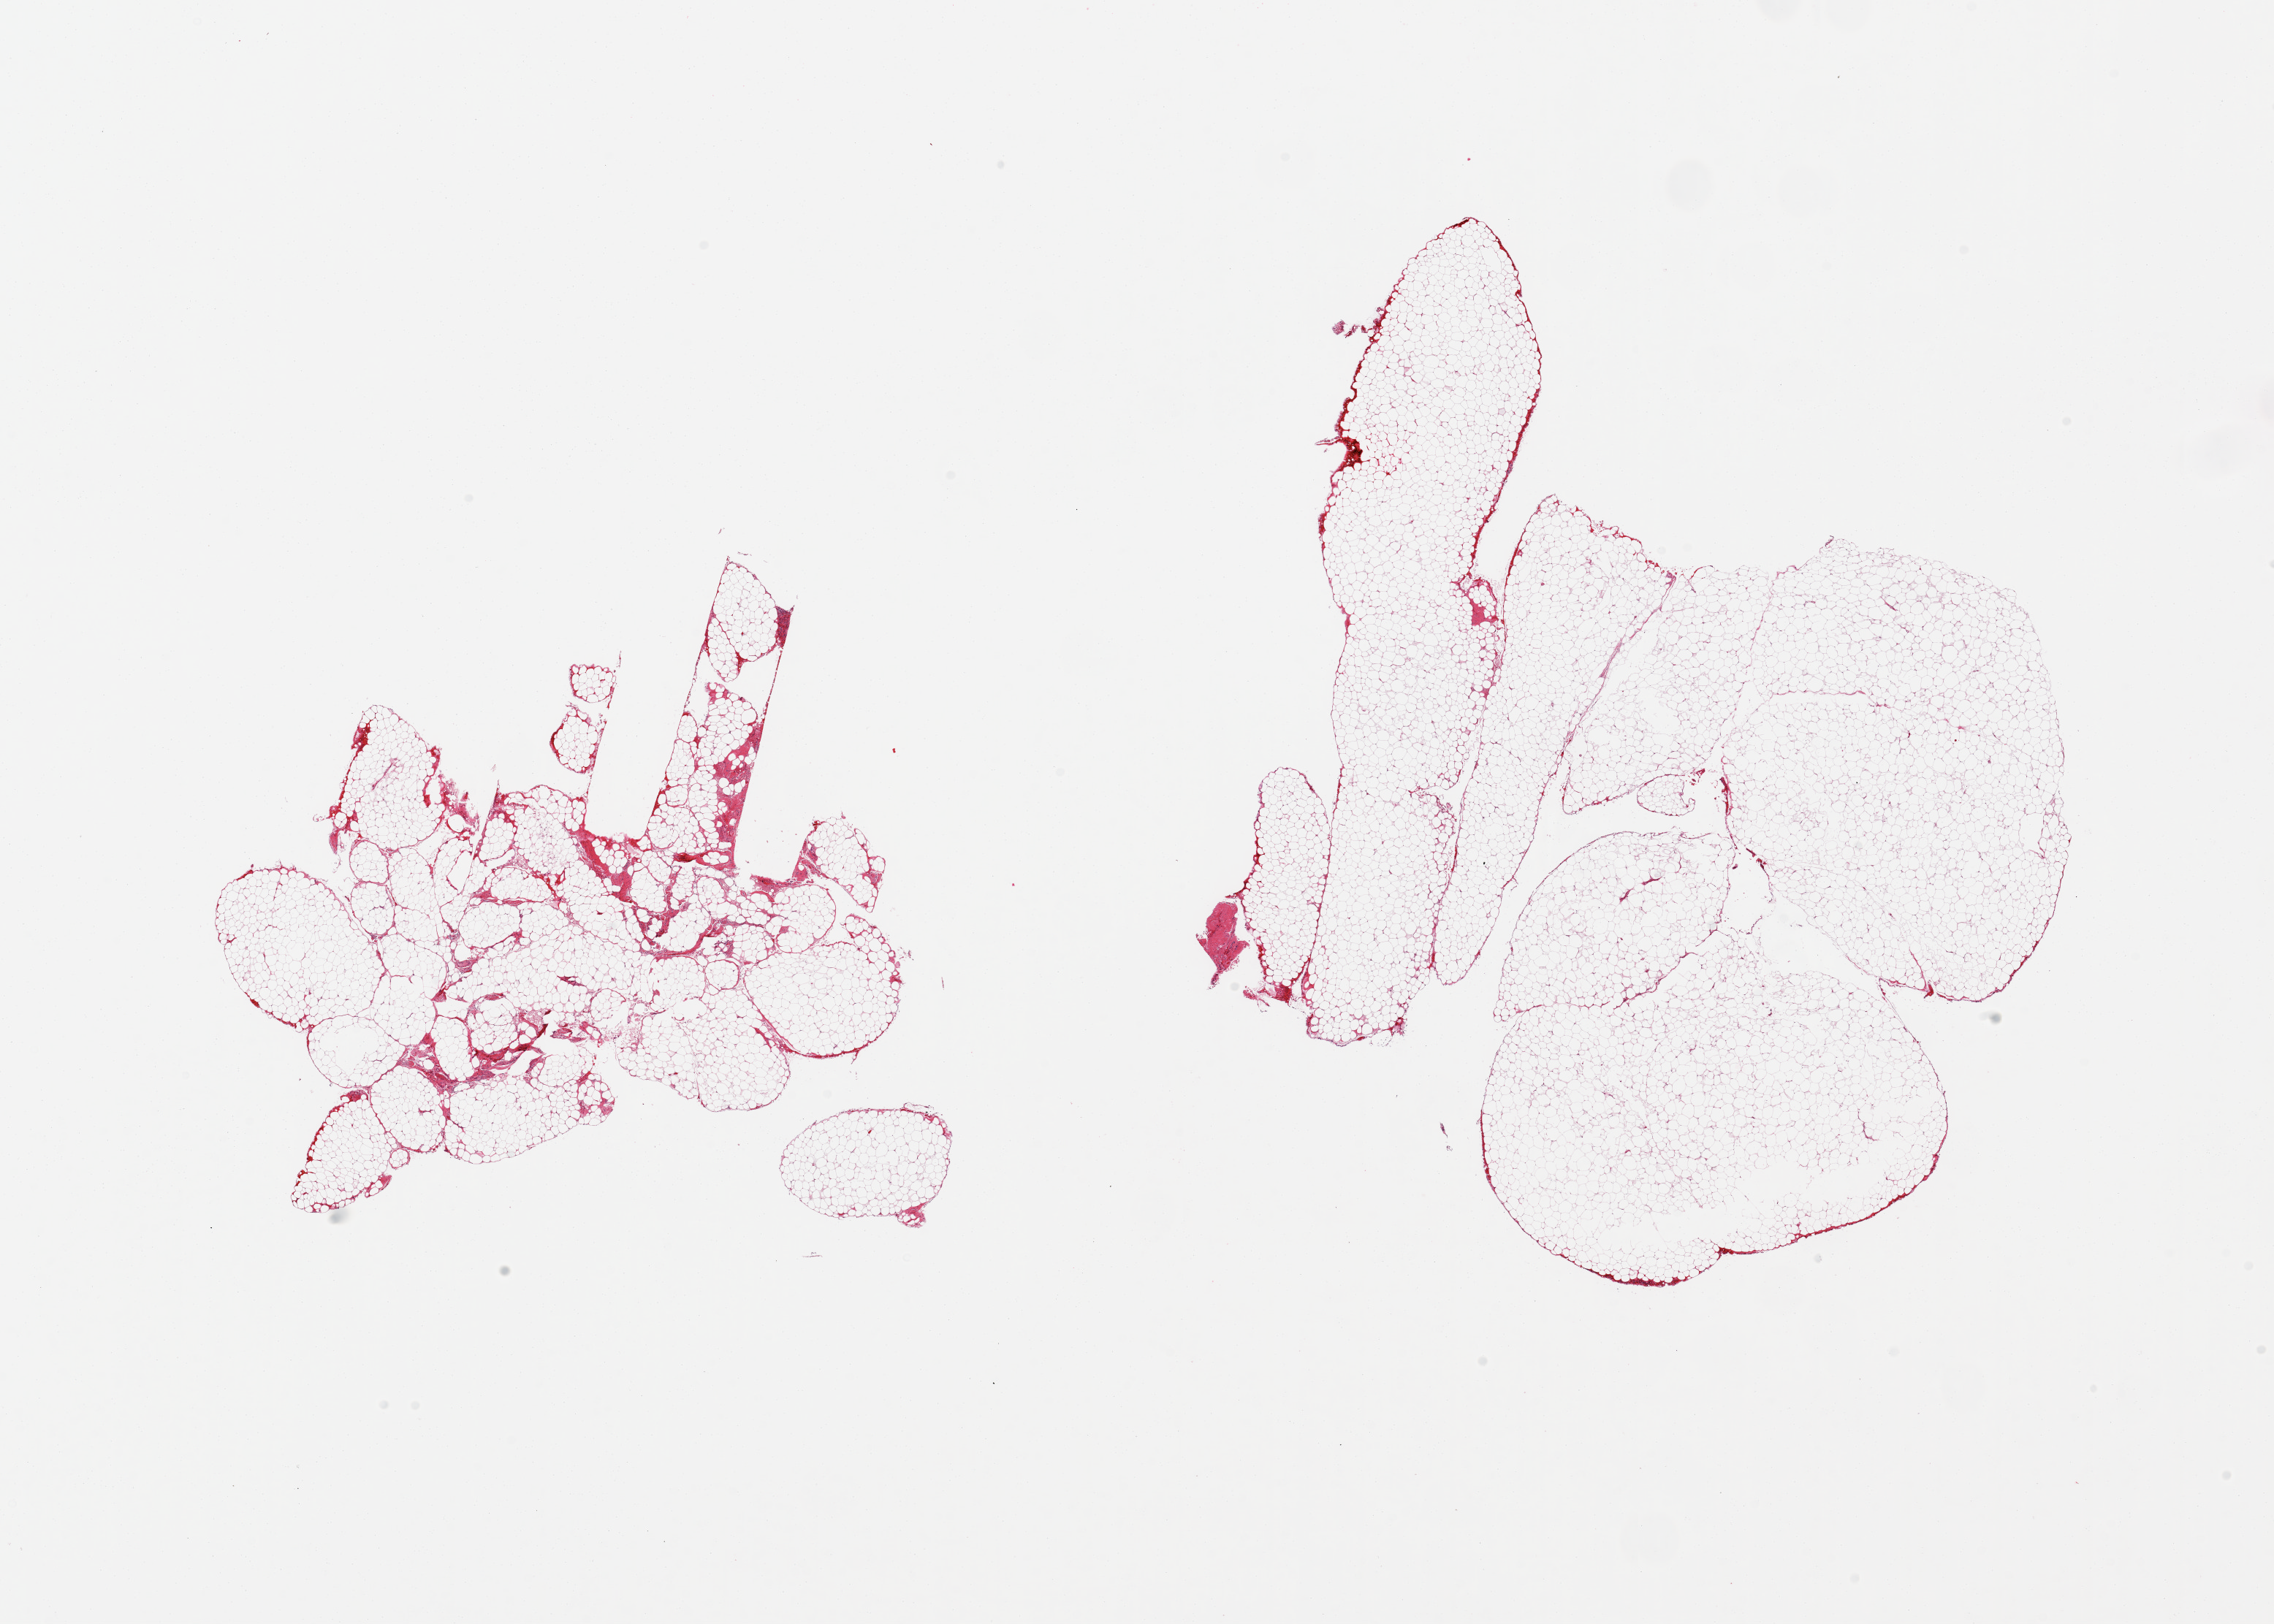
Digitized hematoxylin and eosin (H&E)-stained section, brightfield, a low-resolution overview of the entire scanned area, about 24.6 x 17.6 mm (slide scanned at 20x); PAXgene-fixed, paraffin-embedded tissue; section of omentum (target tissue); donor tissue sample. Donor sex: male.
* review note (as recorded): 2 pieces, ~5-10% fascia